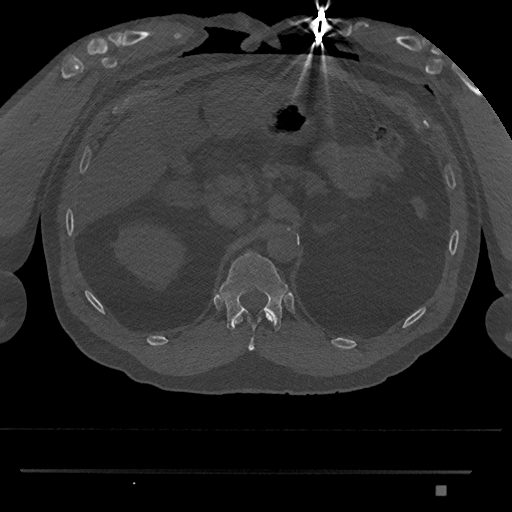
CT including the spine, one axial slice; slice 906 of 1134 in the series (ordered by position); reconstruction kernel Br40s/3; 120 kVp; bone window (W 1800 / L 400 HU); 0.5 mm slice thickness; 512 × 512 image matrix, field of view 429 × 429 mm. Patient: male, 65 years. Case-level facts recorded for this patient, not image findings: primary cancer: prostate.
Annotated regions visible in this slice (semi-automatic segmentation, software-assisted and operator-edited):
- T11 vertebra: bounding box <236,312,272,351> (left, top, right, bottom; pixels)
- T12 vertebra: <219,251,288,331>